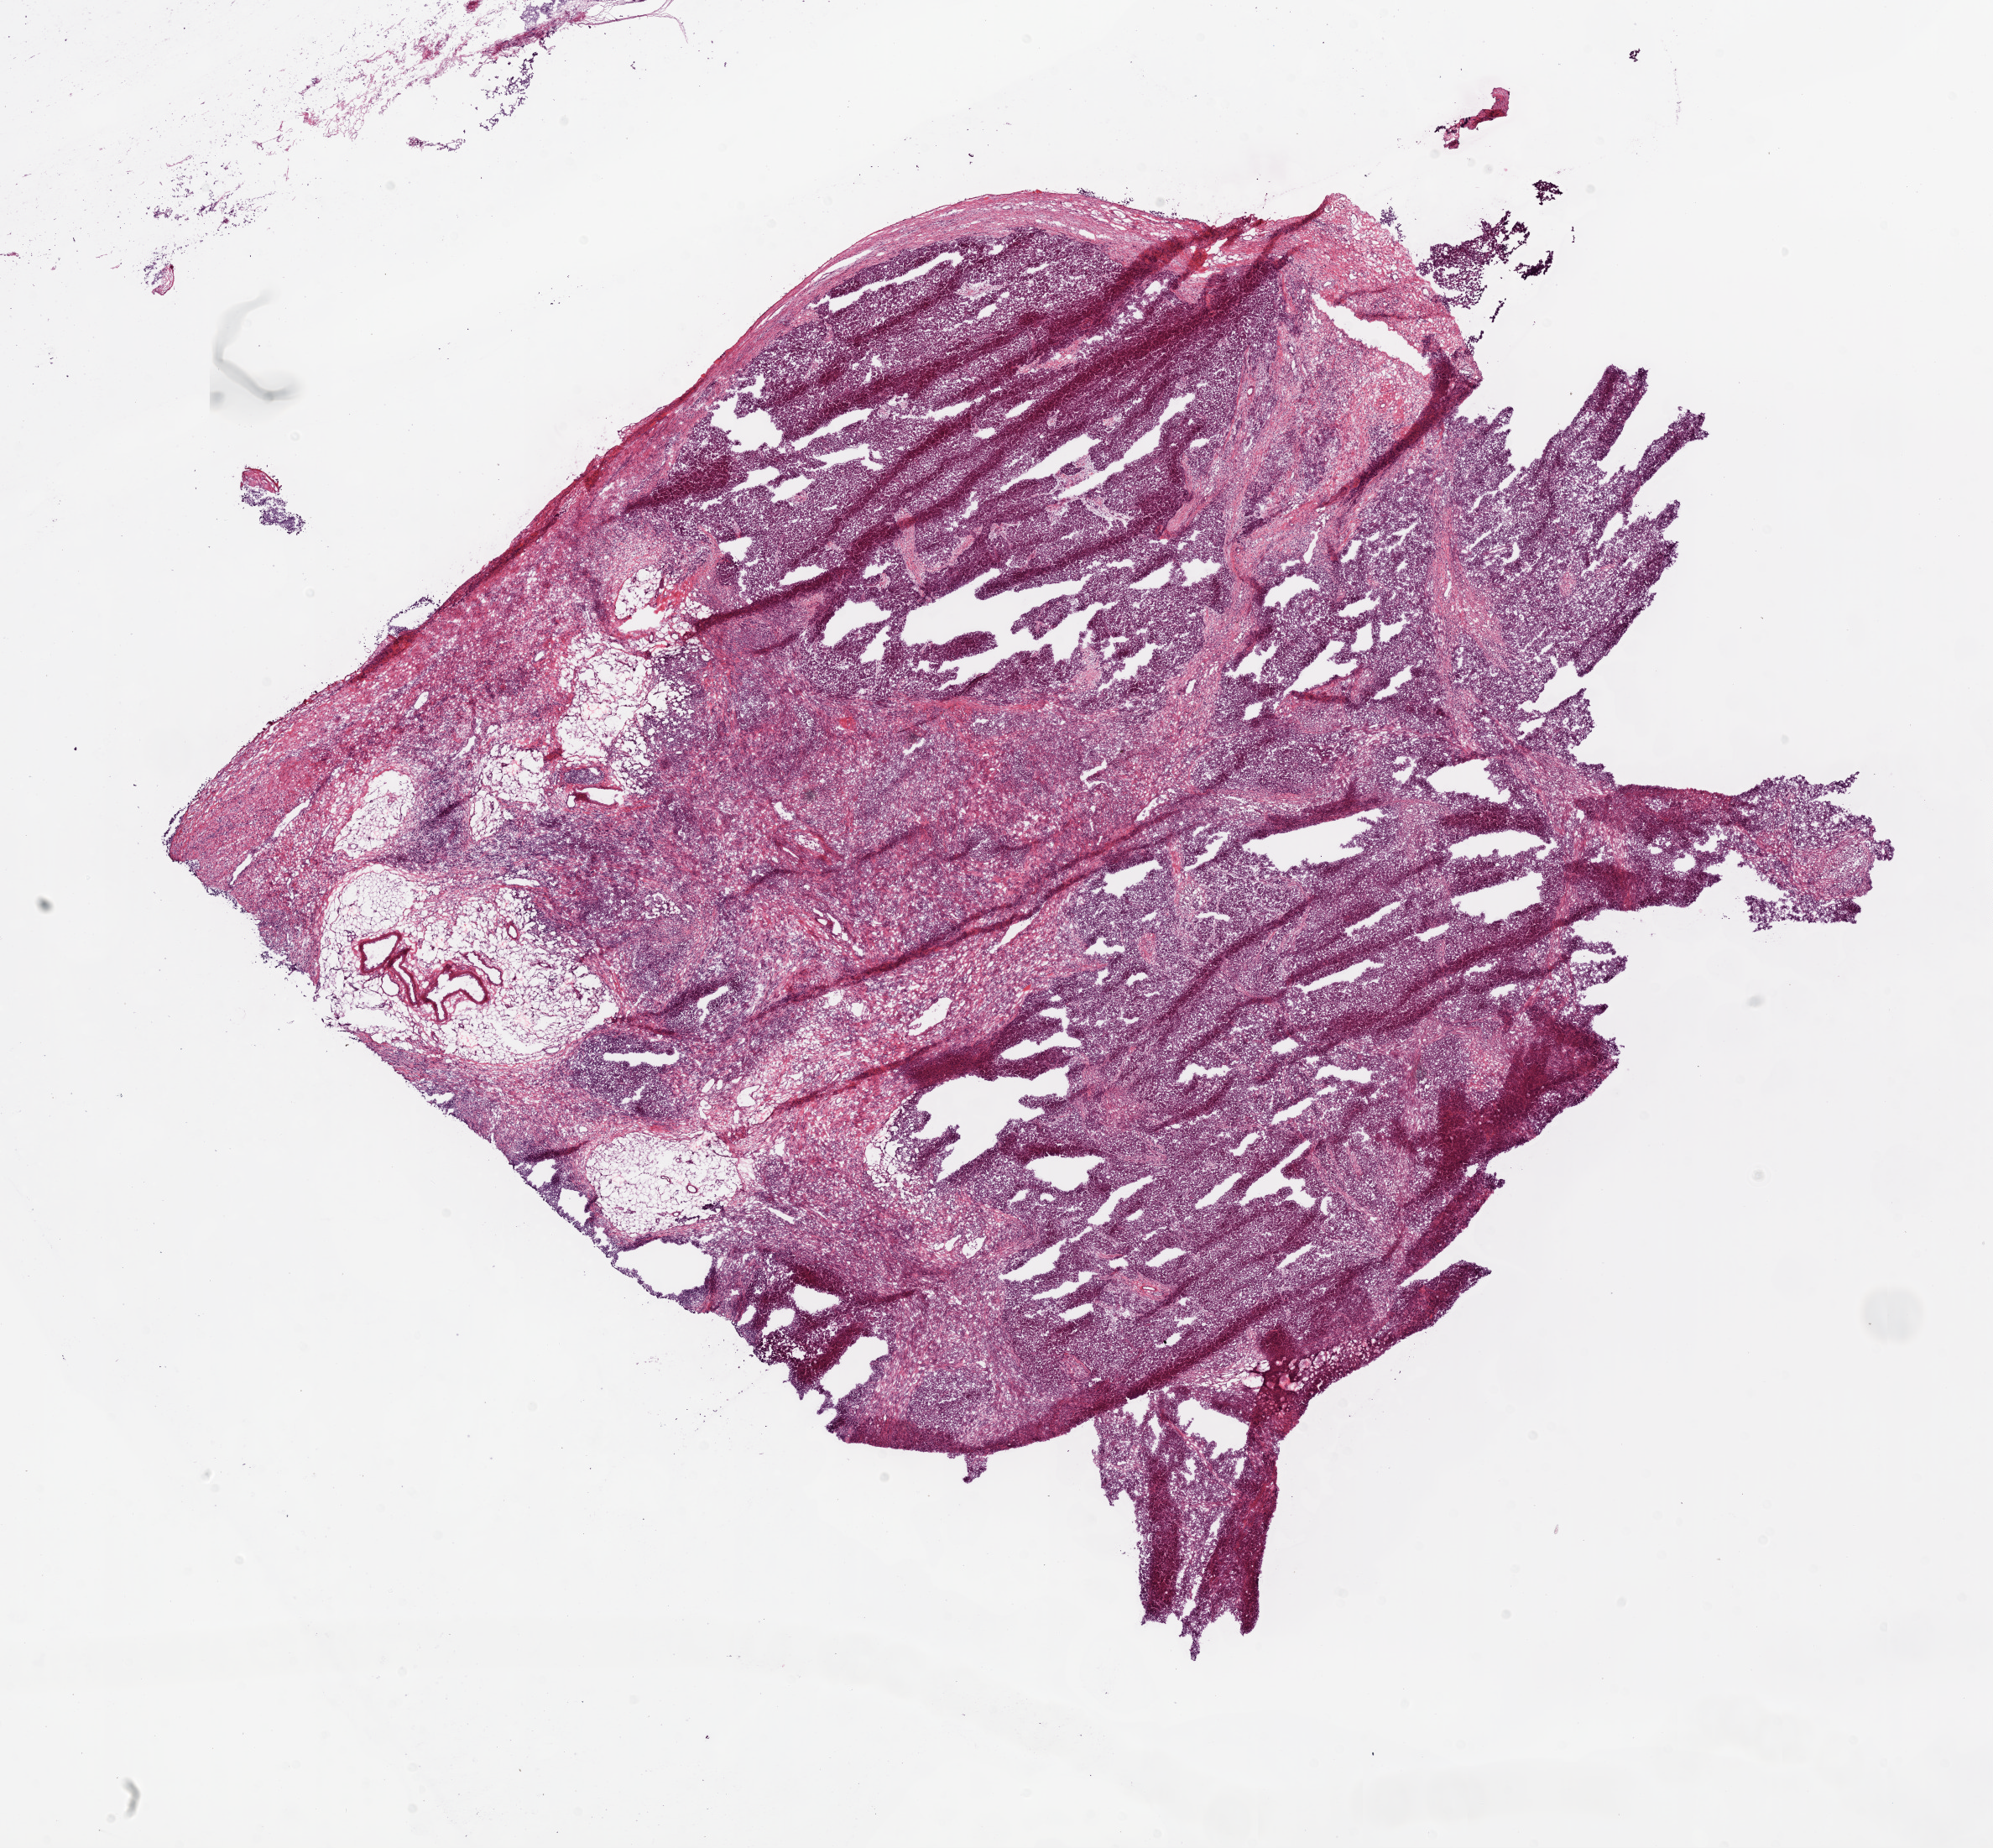
Digitized Hematoxylin and eosin (H&E) stained tissue section (whole slide), a low-resolution overview of the entire scanned area, about 19.1 x 17.7 mm, frozen section, ovary, recurrent tumour sample. Female, age 56 years at initial diagnosis. Slide review estimates, as recorded: tumour cells 80%, tumour nuclei 80%, normal cells 0%, stromal cells 20%, necrosis 0%.
This section: recurrent tumour. Patient diagnosis: Serous cystadenocarcinoma, NOS.